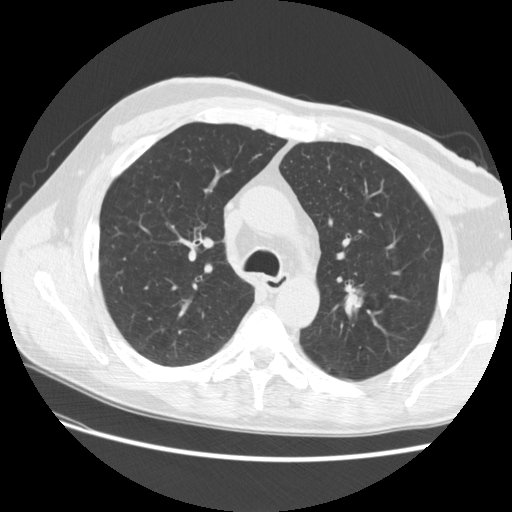
Low-dose screening chest CT, one axial slice. Slice 178 of 256 in the series (ordered by position). Lung window (W 1500 / L -600 HU). 2.5 mm slice thickness. 512 × 512 image matrix, field of view 366 × 366 mm.
Annotated regions visible in this slice (manually delineated by an expert):
- lesion 1 (tumor, upper lobe of left lung): bounding box <346,293,361,310> (left, top, right, bottom; pixels)